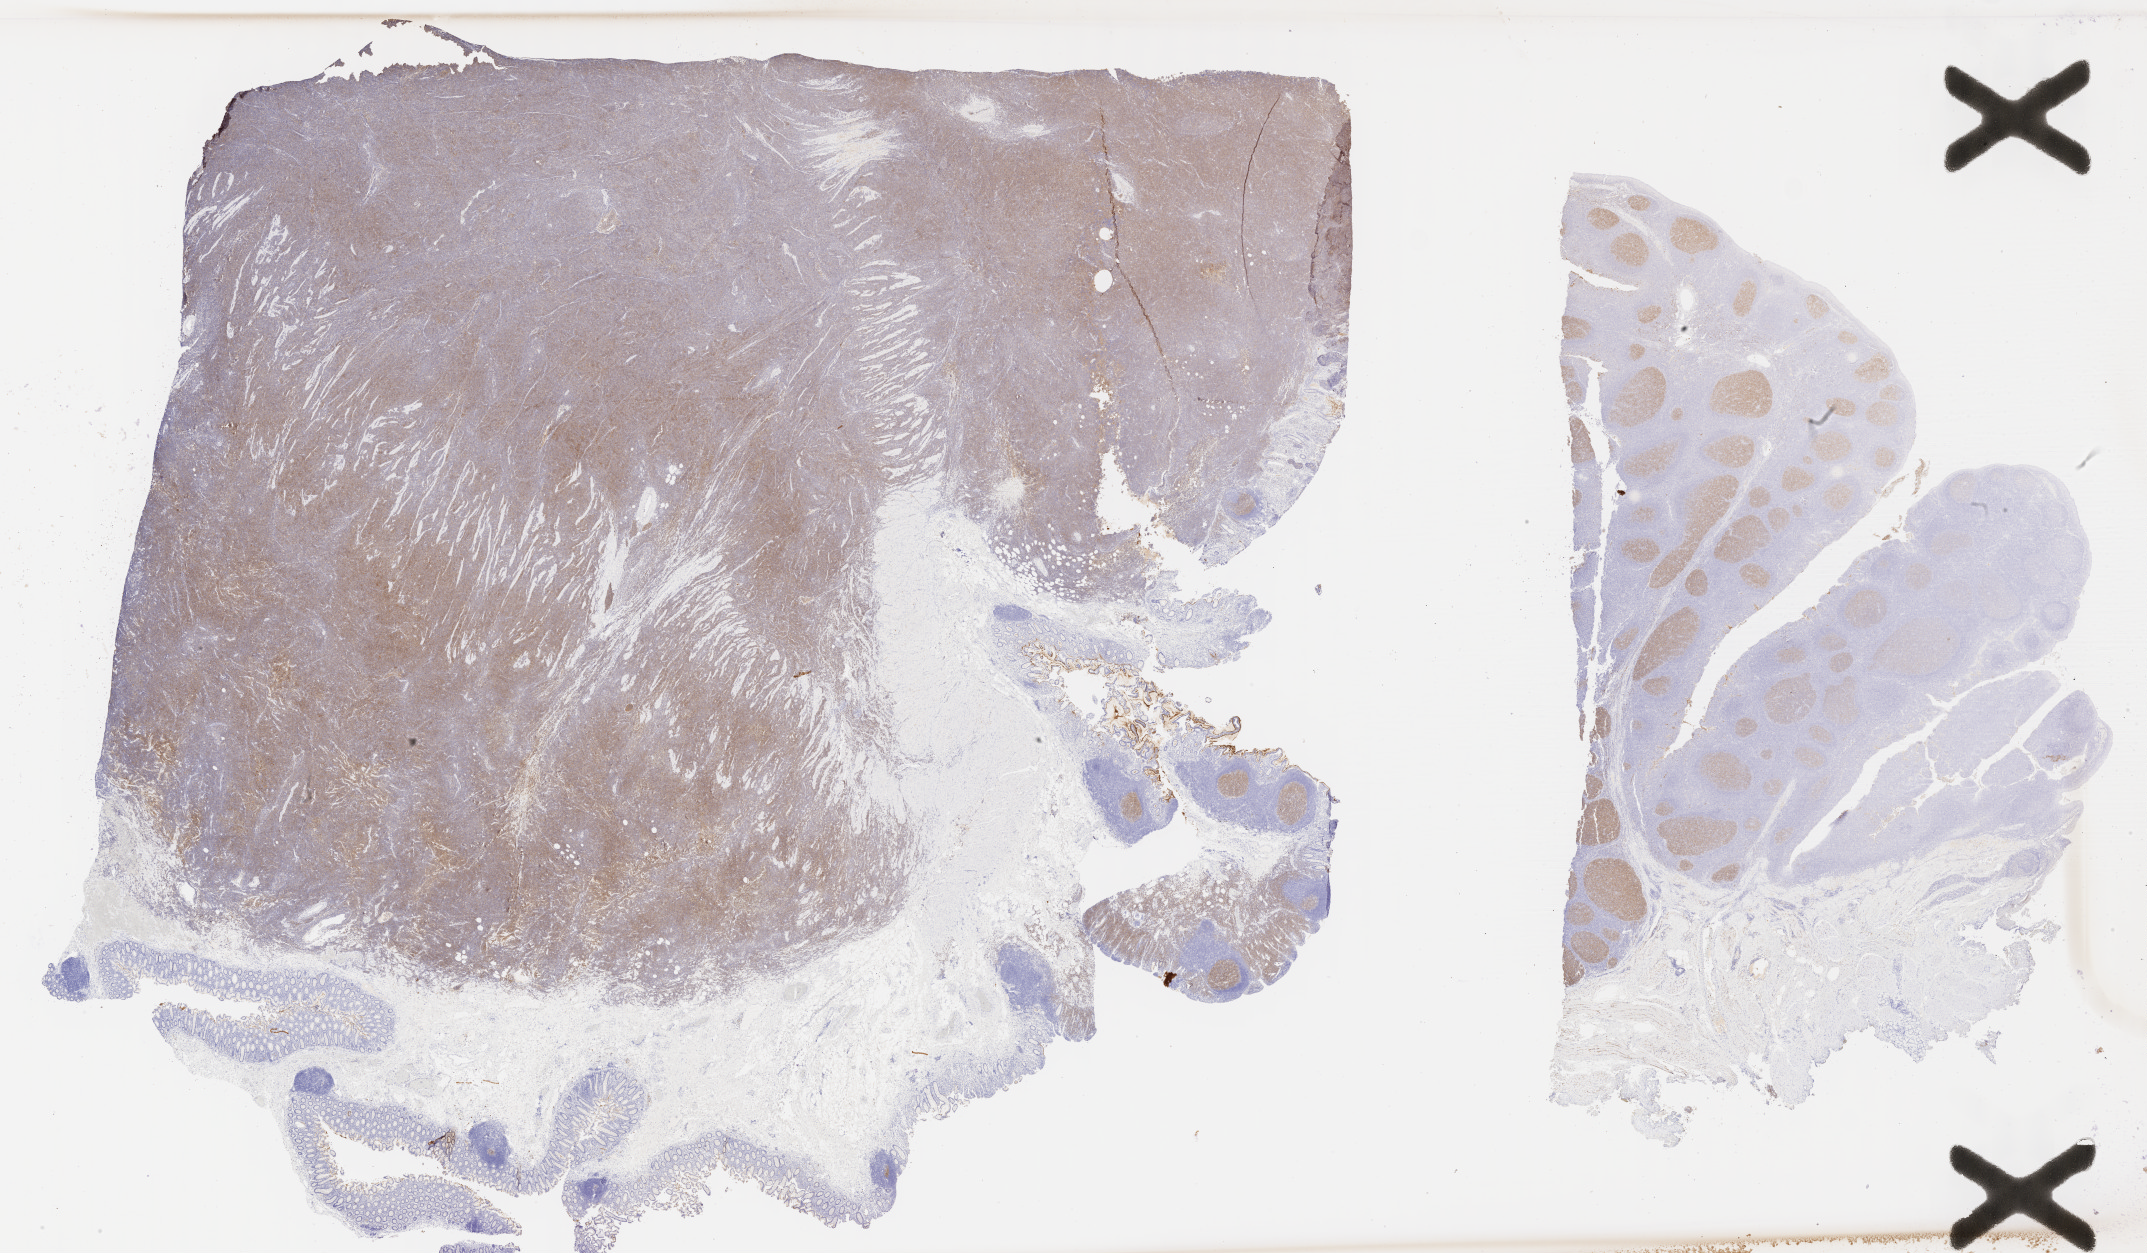
Immunohistochemistry (IHC) whole-slide image stained for CD10 — low-resolution overview of the scanned area, about 34.7 x 20.3 mm, specimen: tumor tissue. Male patient, aged 59.
Histologic diagnosis: Burkitt lymphoma, NOS.